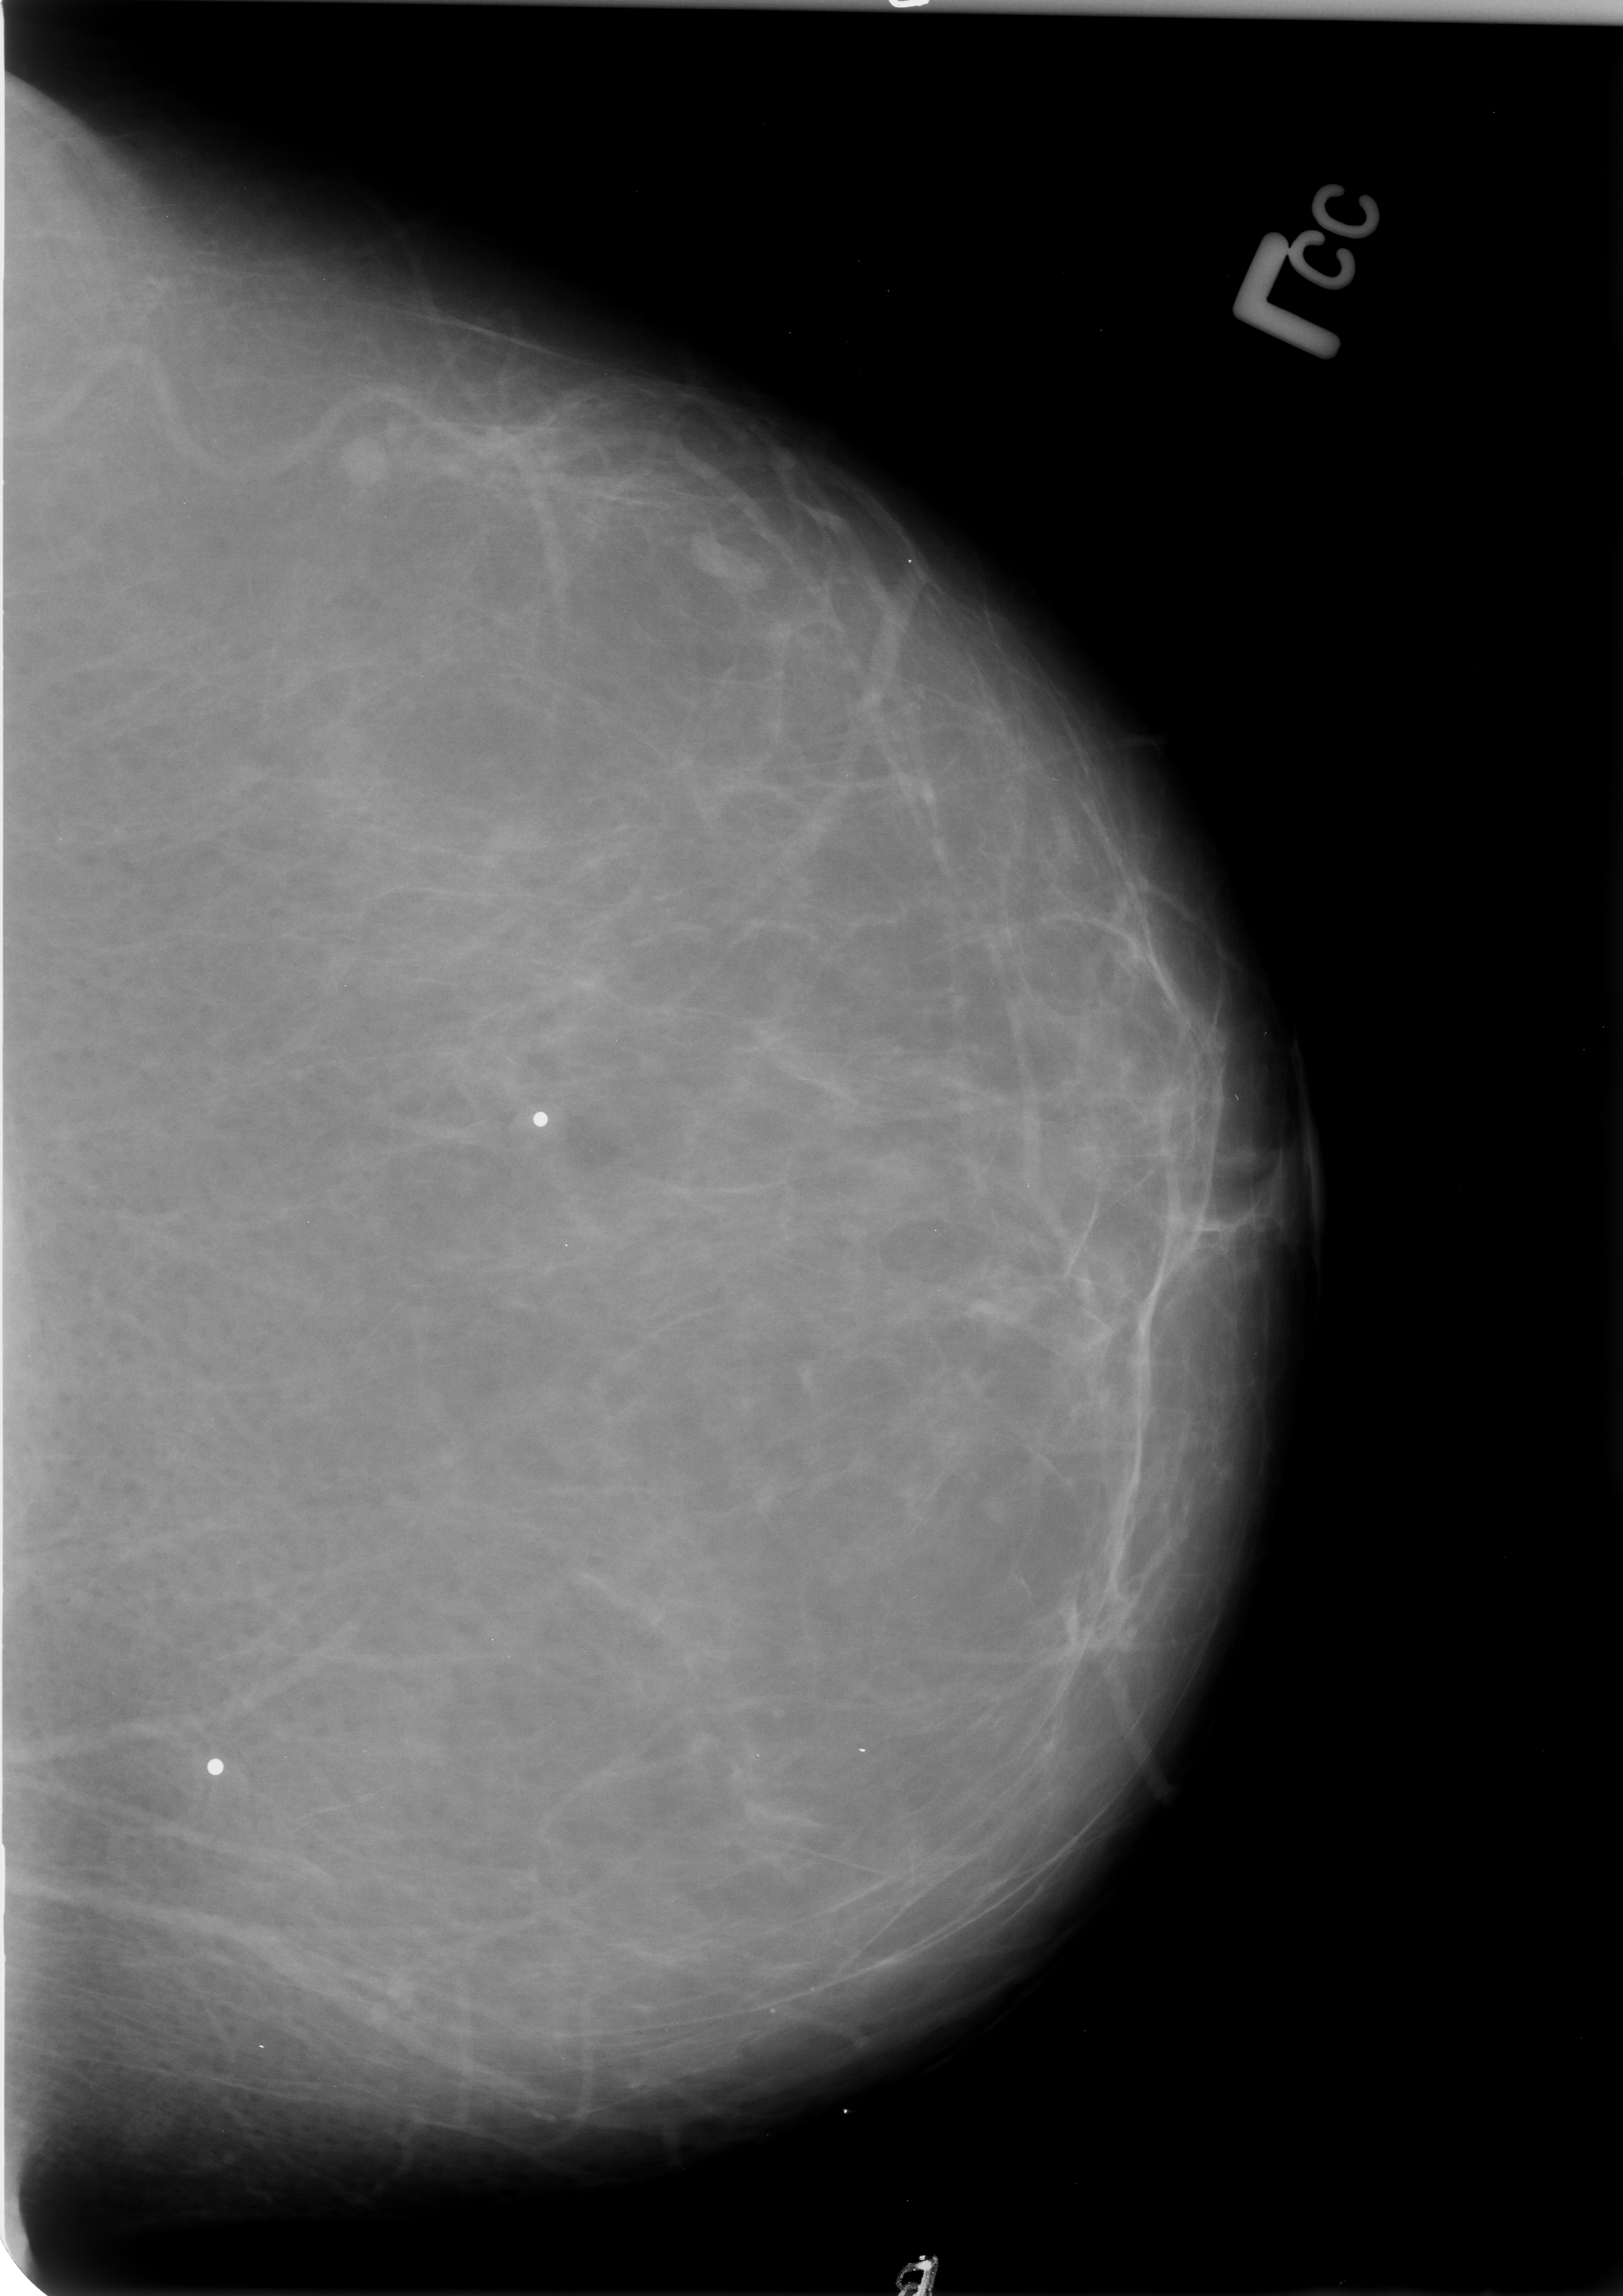
Scanned film-screen mammogram, left breast, craniocaudal (CC) view, breast composition: almost entirely fatty (BI-RADS density category 1 of 4).
Marked findings (only marked abnormalities are described; nothing is implied about the rest of the image): Finding 1 of 2: mass, shape lymph node, margins circumscribed; BI-RADS assessment category 3; benign; no additional work-up was recommended (benign without callback). Finding 2 of 2: mass, shape lymph node, margins circumscribed; BI-RADS assessment category 3; subtlety rating 2 on a 1 (subtle) to 5 (obvious) scale; benign; no additional work-up was recommended (benign without callback).